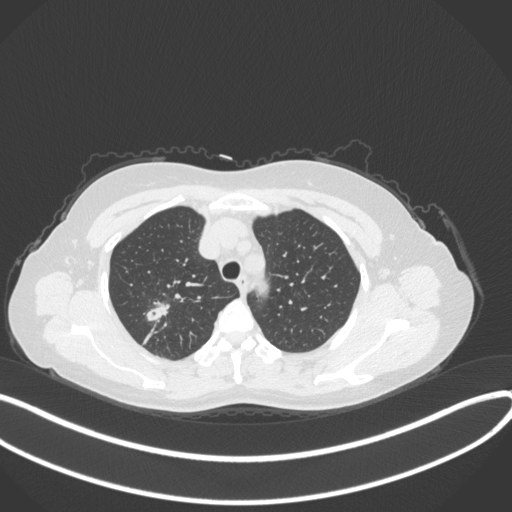
Chest CT, one axial slice; slice 287 of 342 in the series (ordered by position); lung window (W 1500 / L -600 HU); 1 mm slice thickness; 512 × 512 image matrix. Patient: female, 50 years. Case-level facts recorded for this patient, not image findings: clinical TNM (as recorded): T1c N0 M0; histopathological grade: G2-3.
Annotated regions visible in this slice (bounding box drawn by a radiologist):
- lung tumour (recorded histology: adenocarcinoma): bounding box <144,298,172,325> (left, top, right, bottom; pixels)